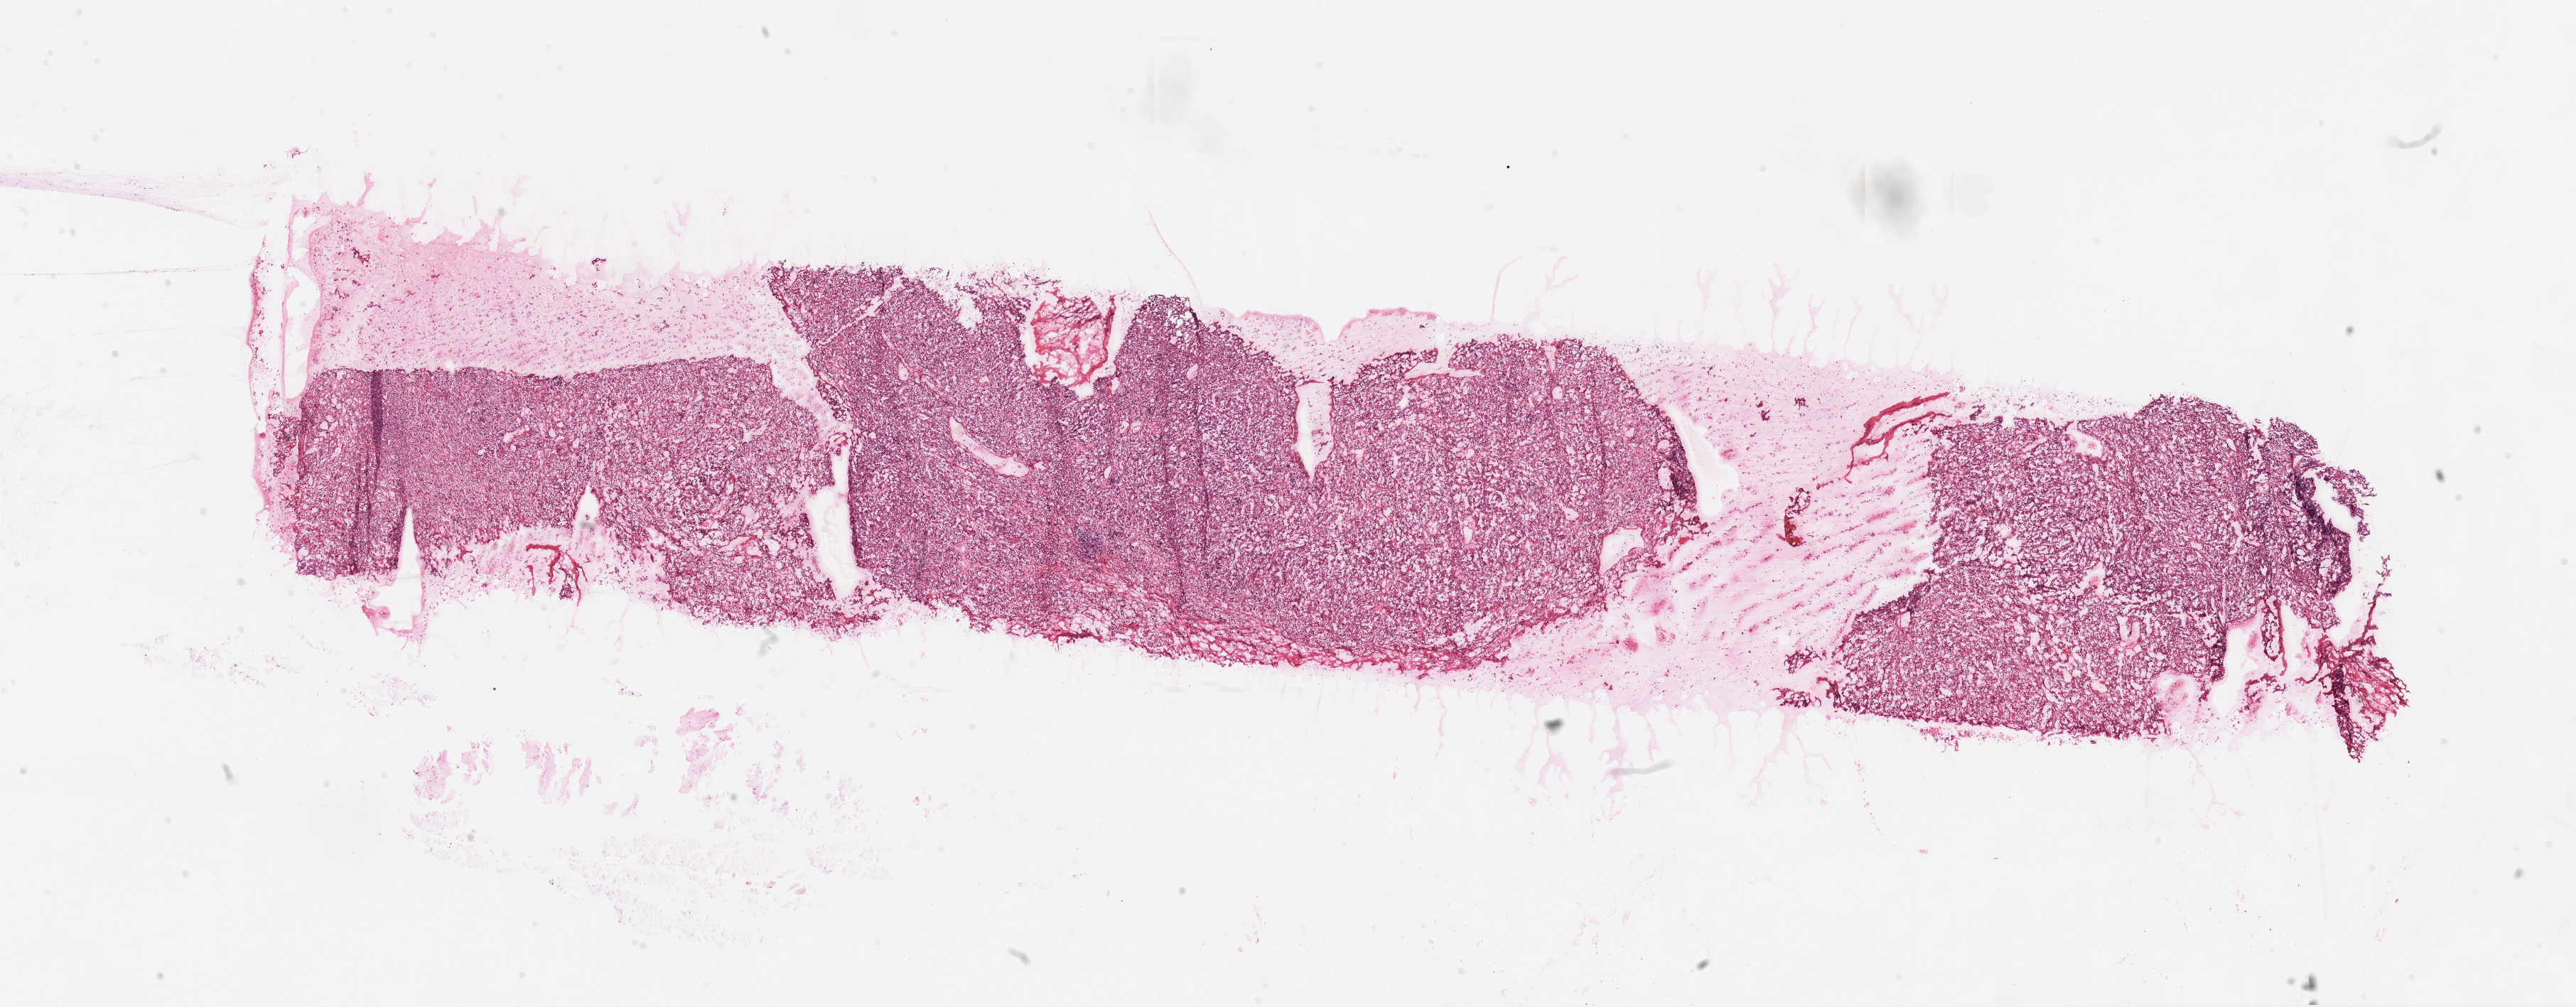
Digitized H&E-stained tissue section (whole slide) — whole scanned area (about 29.1 x 11.4 mm) shown as a low-resolution overview, frozen section from the top of the tissue portion, kidney, primary tumour sample. Female, age 49 years at initial diagnosis. Histologic grade: G2 (moderately differentiated). Composition of this section per pathologist review: tumour cells 95%, tumour nuclei 80%, normal cells 0%, stromal cells 5%, necrosis 0%.
Diagnosis: Clear cell adenocarcinoma, NOS. TNM: T2 N0 M0. AJCC pathologic stage: II.